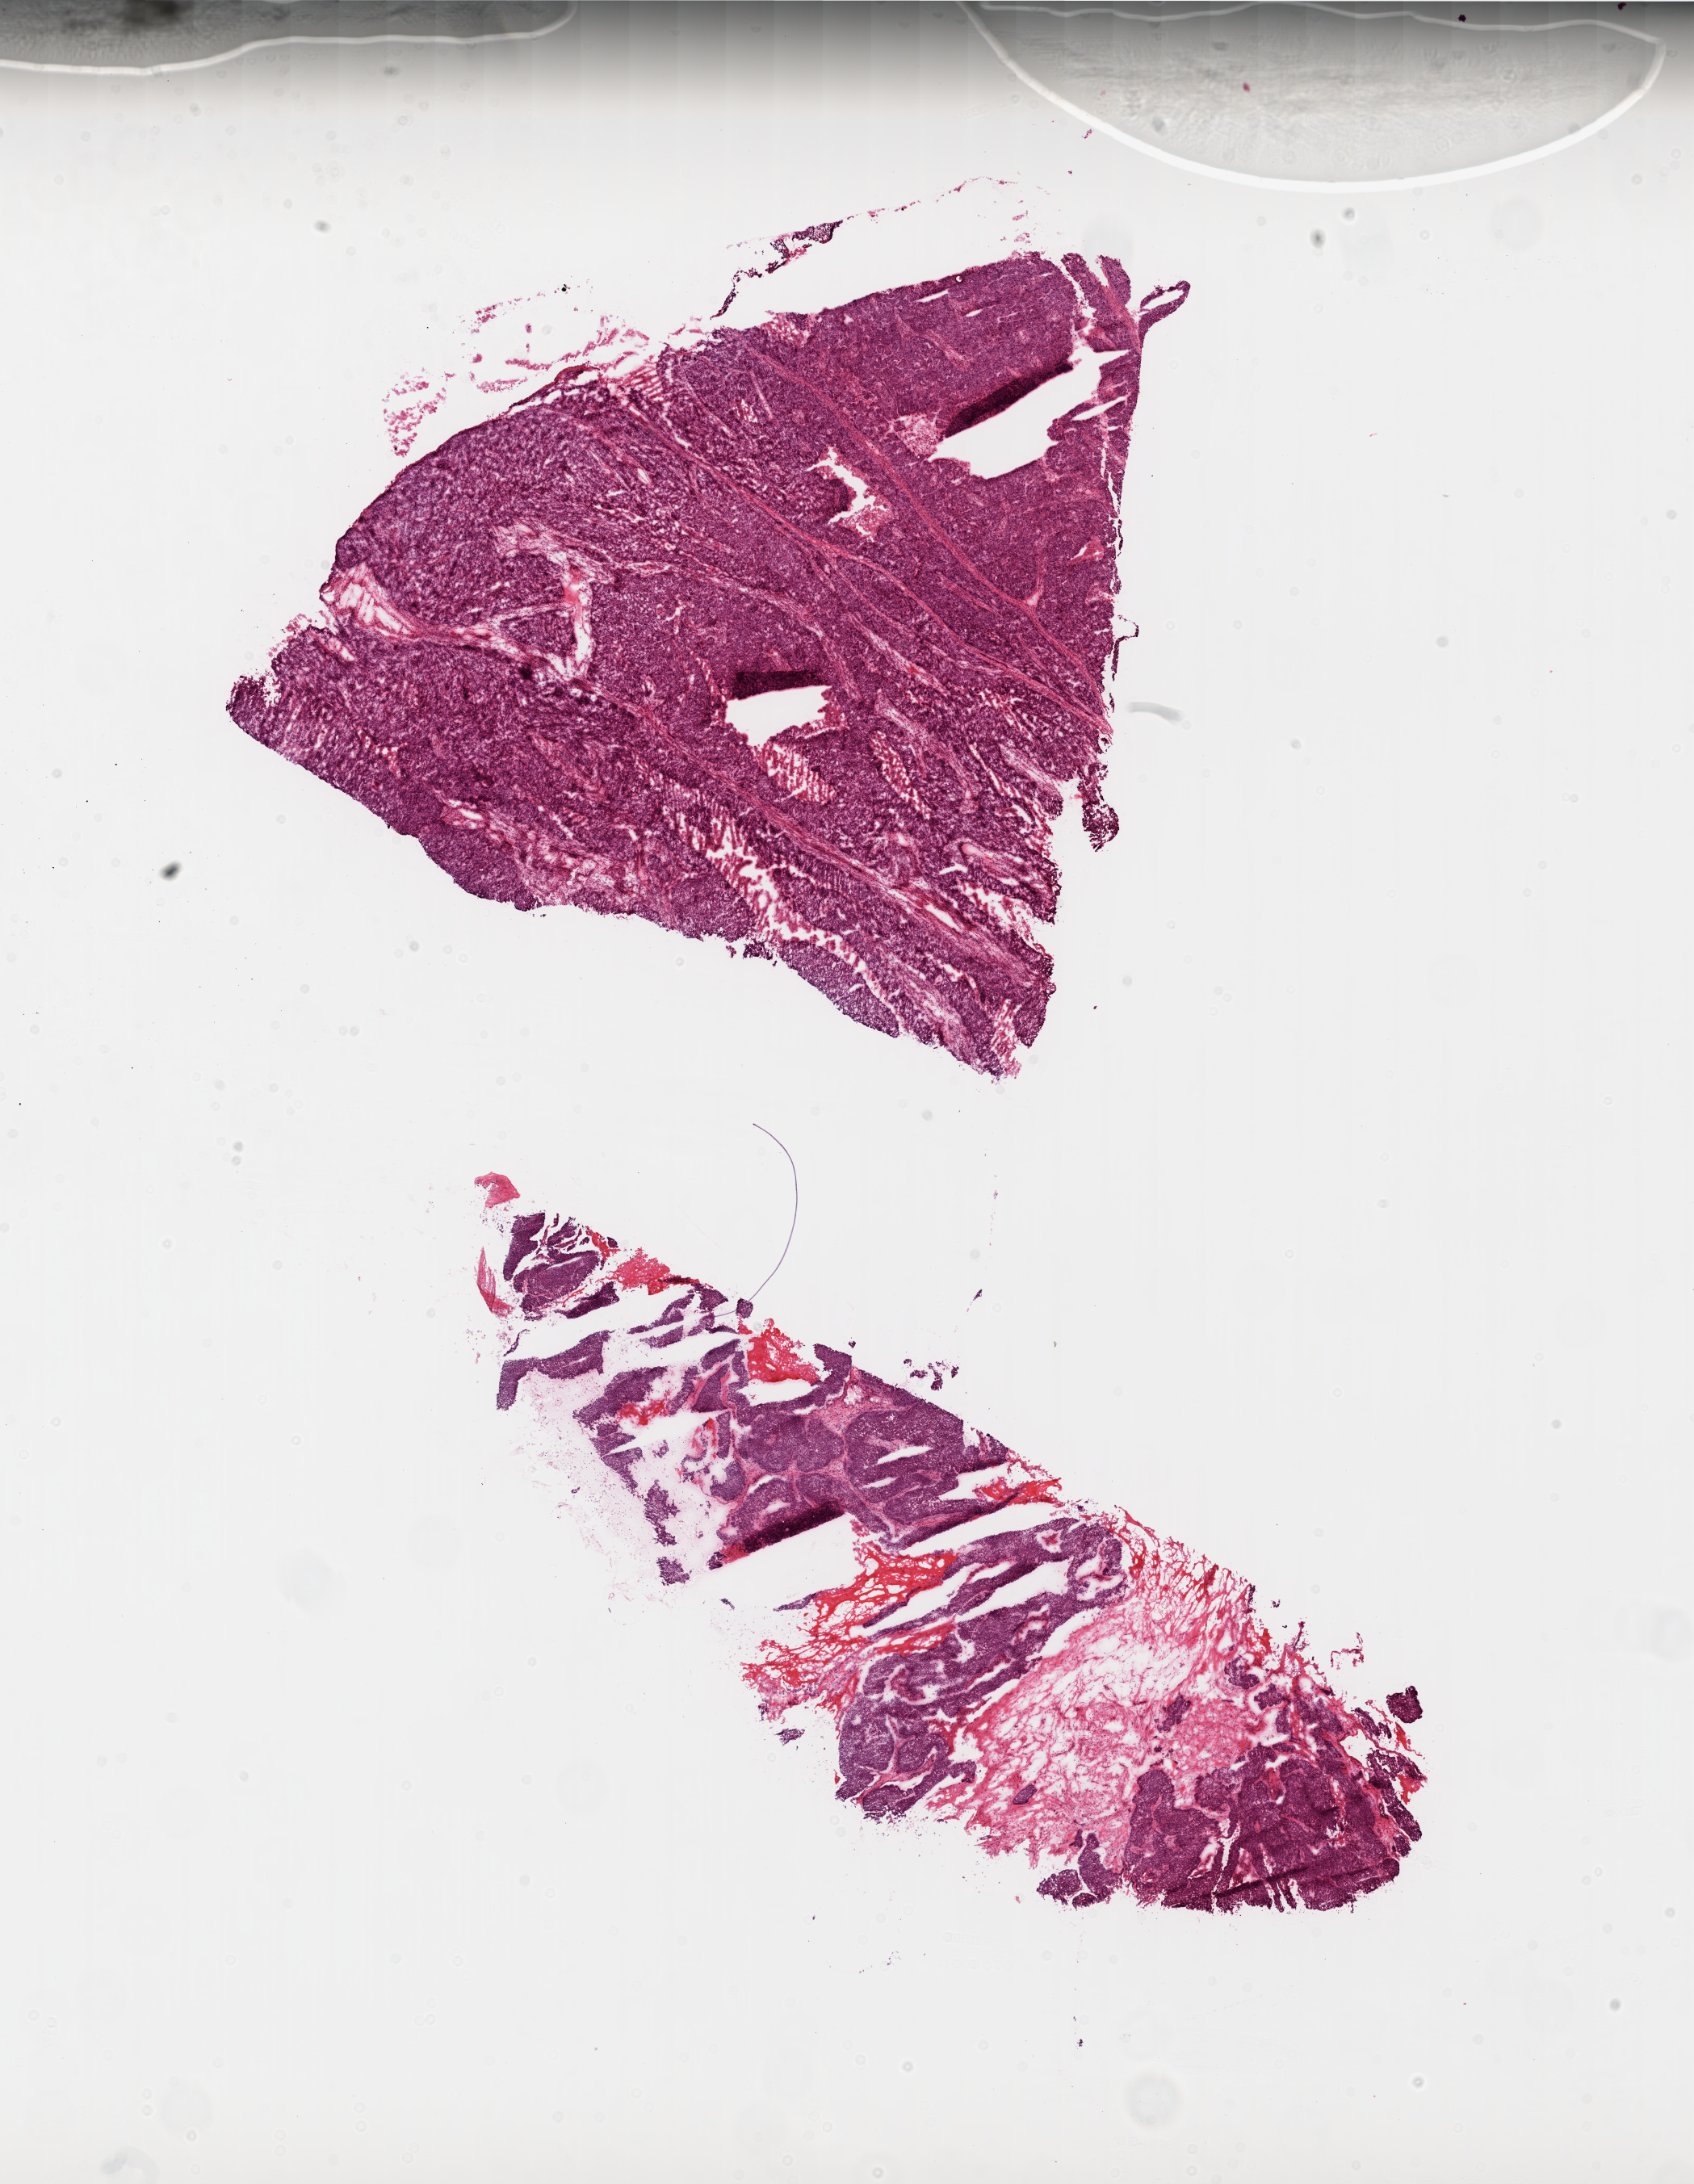
H&E whole-slide image, shown as a low-resolution overview of the whole scanned area (about 16.9 x 21.8 mm, slide scanned at 20x), frozen section from the top of the tissue portion, sample: primary tumour, ovary. Female, age 58 years at initial diagnosis. Histologic grade: G3 (poorly differentiated). Pathologist review of this section (percent, as recorded): tumour cells 85%, tumour nuclei 95%, normal cells 0%, stromal cells 15%, necrosis 0%. Infiltration values recorded for this section: lymphocyte infiltration 50%.
• diagnosis: Serous cystadenocarcinoma, NOS
• laterality: bilateral
• FIGO stage: IIIC